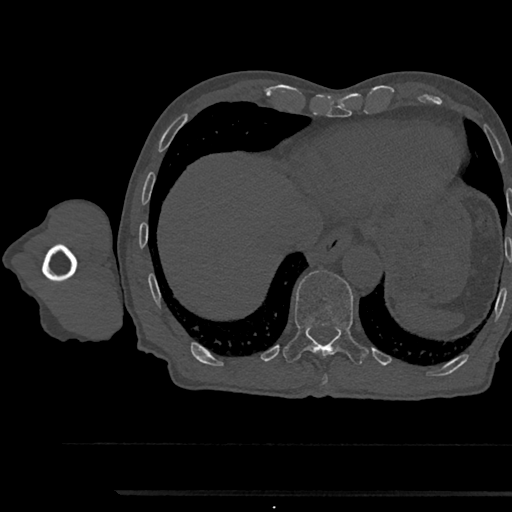
CT including the spine, one axial slice. Slice 796 of 797 in the series (ordered by position). Reconstruction kernel Br40s/3. 120 kVp. Bone window (W 1800 / L 400 HU). 0.5 mm slice thickness. 512 × 512 image matrix, field of view 367 × 367 mm. Patient: male, 79 years. Case-level facts recorded for this patient, not image findings: primary cancer: prostate.
Annotated regions visible in this slice (semi-automatic segmentation, software-assisted and operator-edited):
- T11 vertebra: bounding box (x1, y1, x2, y2) in pixels: (282, 271, 368, 360)